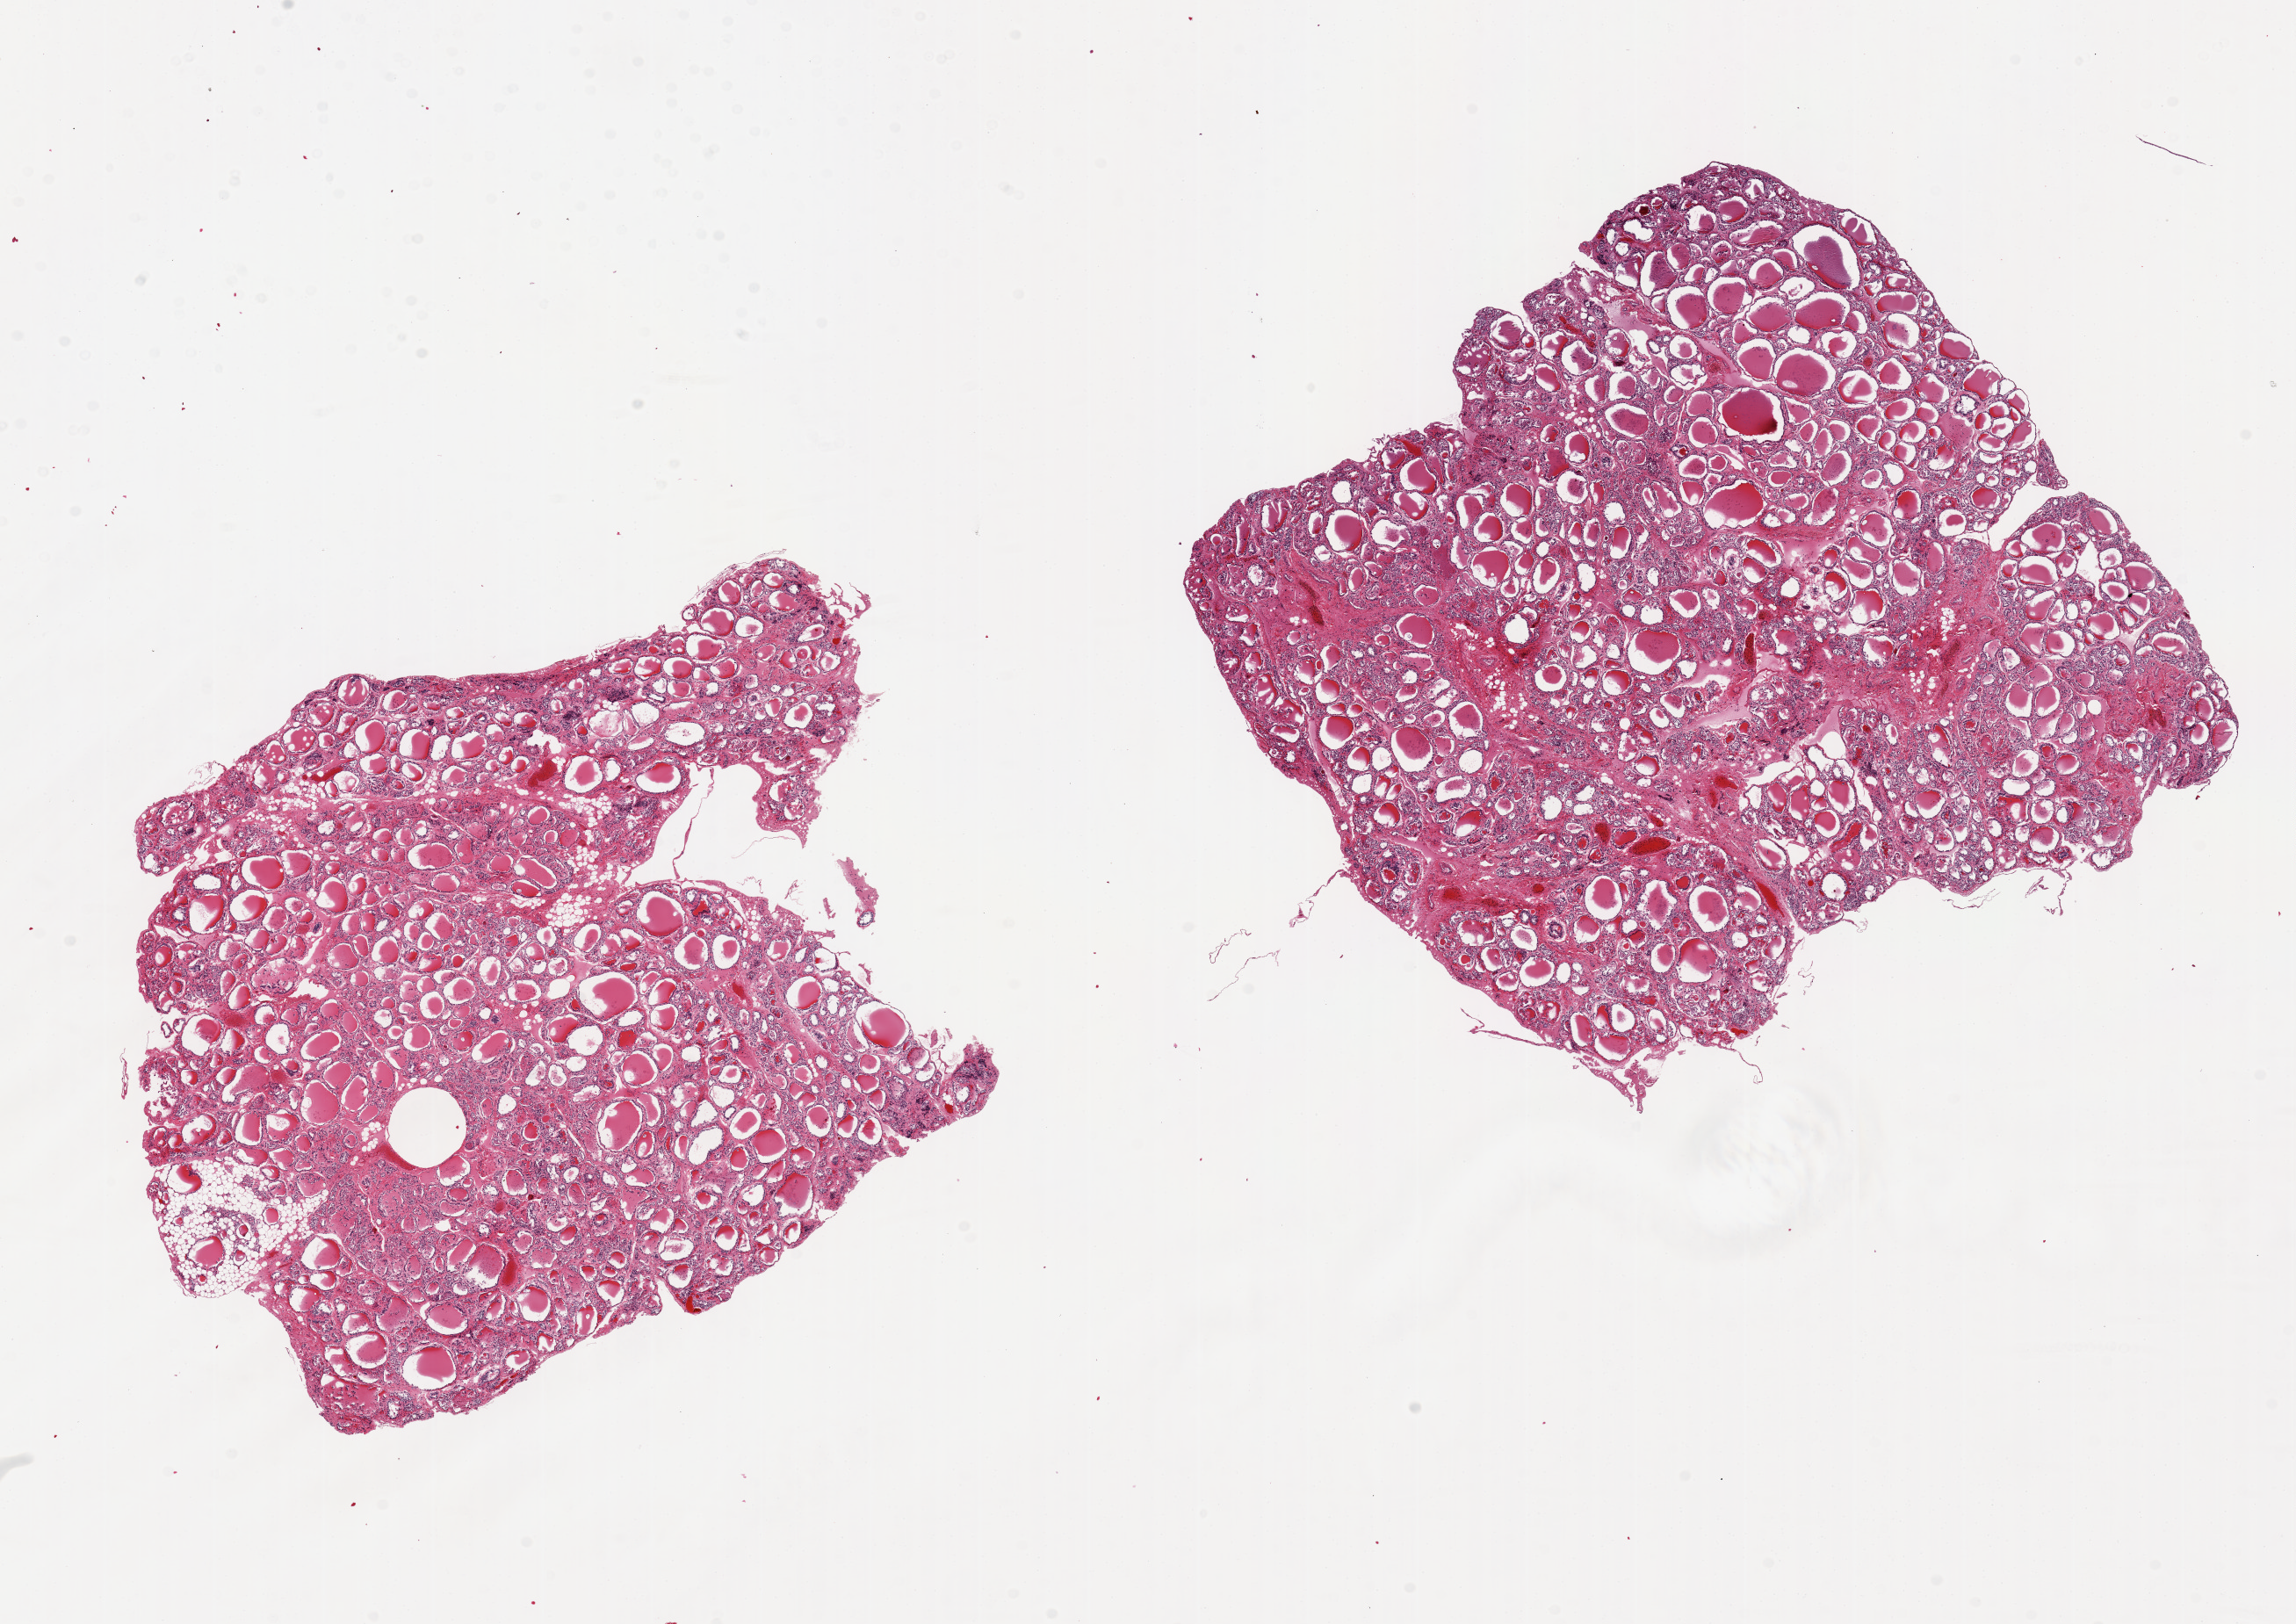
Whole-slide image, haematoxylin and eosin stain — shown as a low-resolution overview of the whole scanned area (about 20.7 x 14.6 mm), PAXgene-fixed paraffin-embedded (PFPE) section, sampled site (target tissue): thyroid, tissue donor sample. Male donor.
* reviewer comment on this tissue sample: 2 pieces, 6x7 & 6.7x7.3mm